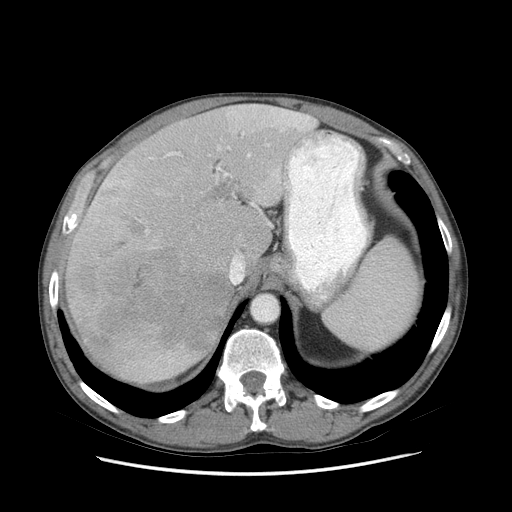
Contrast-enhanced abdominal CT (liver protocol), one axial slice. Slice 58 of 89 in the series (ordered by position). Soft-tissue window (W 400 / L 40 HU). 2.5 mm slice thickness. 512 × 512 image matrix, field of view 380 × 380 mm. From the clinical record (not read from this slice): diagnosis: hepatocellular carcinoma (patient treated with transarterial chemoembolisation; whether this scan precedes or follows treatment is not stated here); TNM stage (as recorded): Stage-IIIB; Child-Pugh class: A.
Outlined on this slice (semi-automatically segmented with operator editing):
- liver parenchyma outside the tumour (the mass and vessels are separate outlines, so this box may not span the whole liver): bounding box (x1, y1, x2, y2) in pixels: (64, 104, 314, 382)
- mass: (68, 212, 226, 366)
- liver vessels: (93, 105, 311, 267)